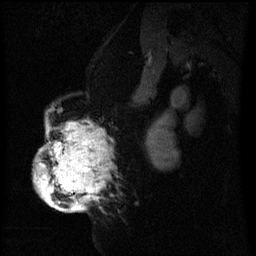
Breast MRI (dynamic contrast-enhanced), one sagittal slice. Position 38 of 60 along the scan axis. Dynamic contrast-enhanced series, image 2 of 3 at this slice position (ordered by acquisition). 1.5 T. TE 4.2 ms, TR 8 ms. 256 × 256 image matrix, field of view 200 × 200 mm. Patient: female, 50 years.
Annotated regions visible in this slice (semi-automatically segmented with operator editing):
- analysis volume of interest (the breast-tissue region the enhancement analysis was run in; not a lesion): box from (x=35, y=116) to (x=111, y=211) px
- tumour enhancement mask (voxels above the 70 % enhancement threshold inside the analysis volume of interest): (x=36, y=124)–(x=103, y=211)